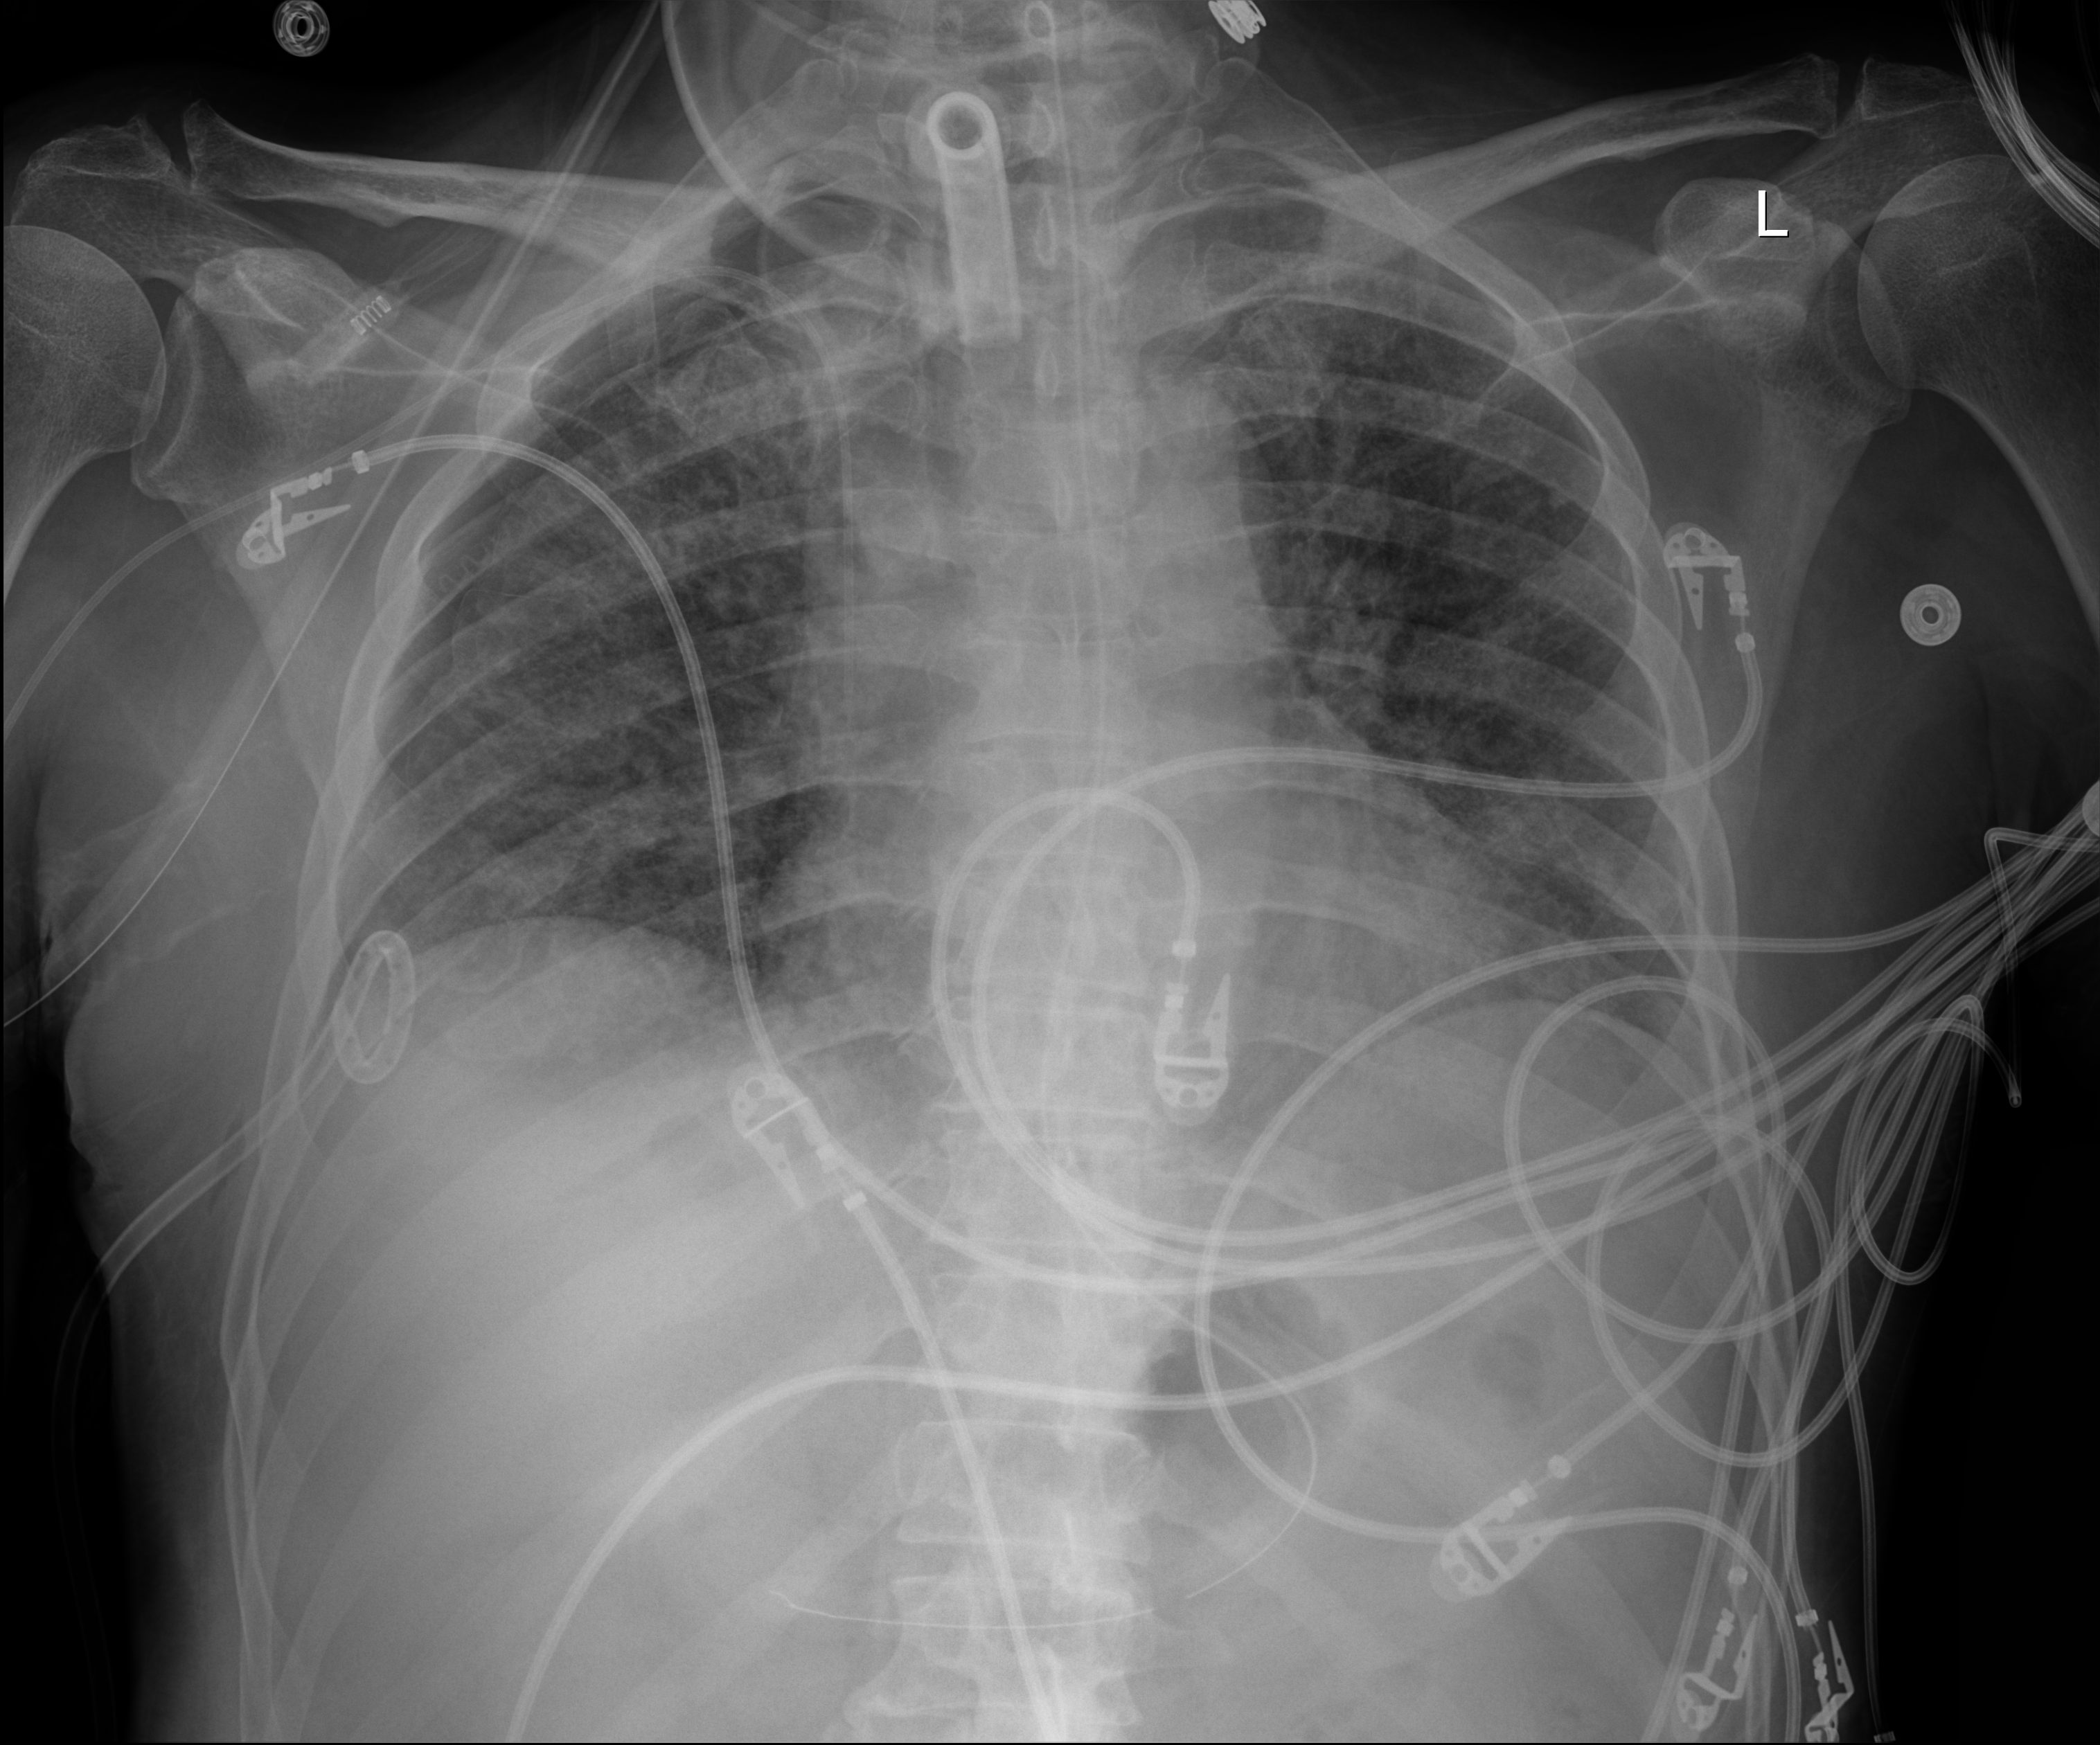
Portable chest radiograph. Patient hospitalised with COVID-19; male, aged 18–59 years.
From the hospital-stay record, not from the radiograph (when in the stay this image was taken is not recorded): length of hospital stay: 77 days; other chronic lung disease (admission record): no.